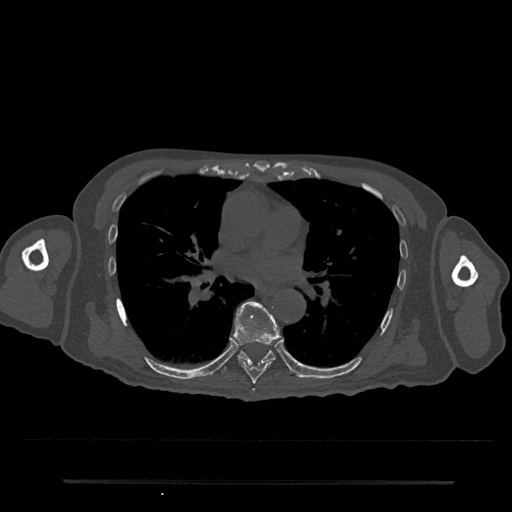
CT including the spine, one axial slice. 120 kVp. Bone window (W 1800 / L 400 HU). 0.5 mm slice thickness. 512 × 512 image matrix. Male patient, age 74 years. Case-level facts recorded for this patient, not image findings: primary cancer: prostate.
Annotated regions visible in this slice (semi-automatic segmentation, software-assisted and operator-edited):
- T6 vertebra: bounding box (x1, y1, x2, y2) in pixels: (253, 389, 255, 392)
- T7 vertebra: (234, 301, 282, 384)
- T8 vertebra: (222, 350, 289, 374)